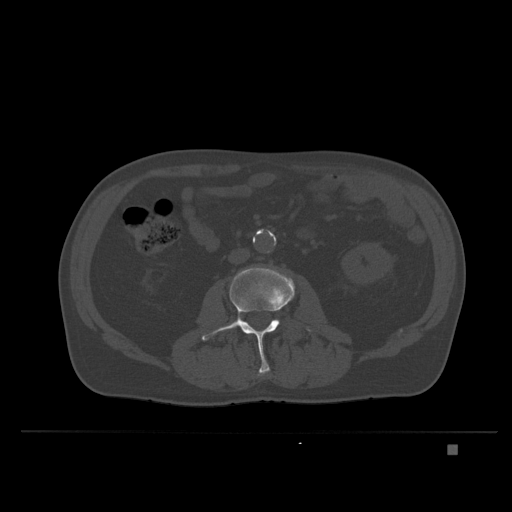
CT including the spine, one axial slice. Slice 96 of 435 in the series (ordered by position). Bone window (W 1800 / L 400 HU). 1.5 mm slice thickness. 512 × 512 image matrix, field of view 434 × 434 mm. Patient: male, 73 years. From the clinical record (not read from this slice): primary cancer: skin.
Annotated regions visible in this slice (semi-automatically segmented with operator editing):
- L2 vertebra: bounding box <258,370,270,376> (left, top, right, bottom; pixels)
- L3 vertebra: <201,266,312,373>